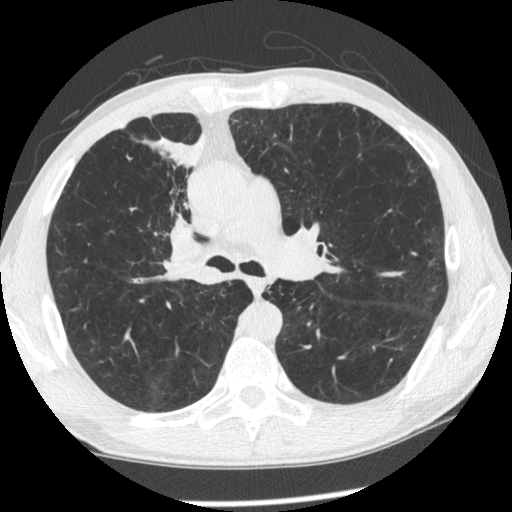
Low-dose screening chest CT, one axial slice; position 145 of 261 along the scan axis; reconstruction kernel STANDARD; 120 kVp; lung window (W 1500 / L -600 HU); 1.25 mm slice thickness; 512 × 512 image matrix.
Structures marked on this image (expert manual segmentation):
- lesion 1 (tumor, upper lobe of right lung): box from (x=145, y=134) to (x=206, y=236) px